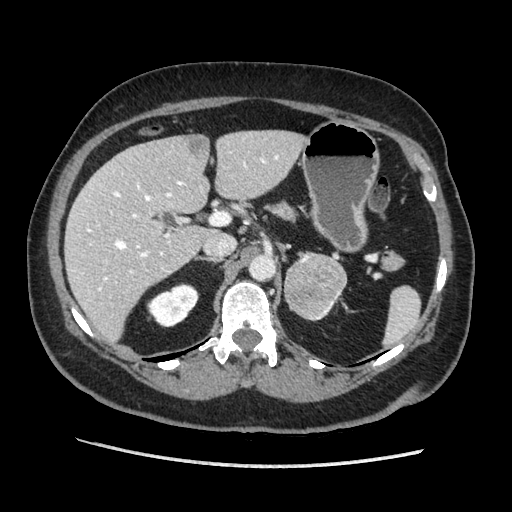
Contrast-enhanced abdominal CT, one axial slice. Slice 123 of 203 in the series (ordered by position). Soft-tissue window (W 400 / L 40 HU). 1.25 mm slice thickness. 512 × 512 image matrix, field of view 360 × 360 mm. Female patient. Case-level facts recorded for this patient, not image findings: diagnosis: adrenocortical carcinoma; tumour side: left adrenal; tumour size at pathology: 6.5 cm; Ki-67 index: 22 %; stage (as recorded): 2.
Structures marked on this image (semi-automatic segmentation, software-assisted and operator-edited):
- mass: bounding box (x1, y1, x2, y2) in pixels: (285, 252, 348, 320)